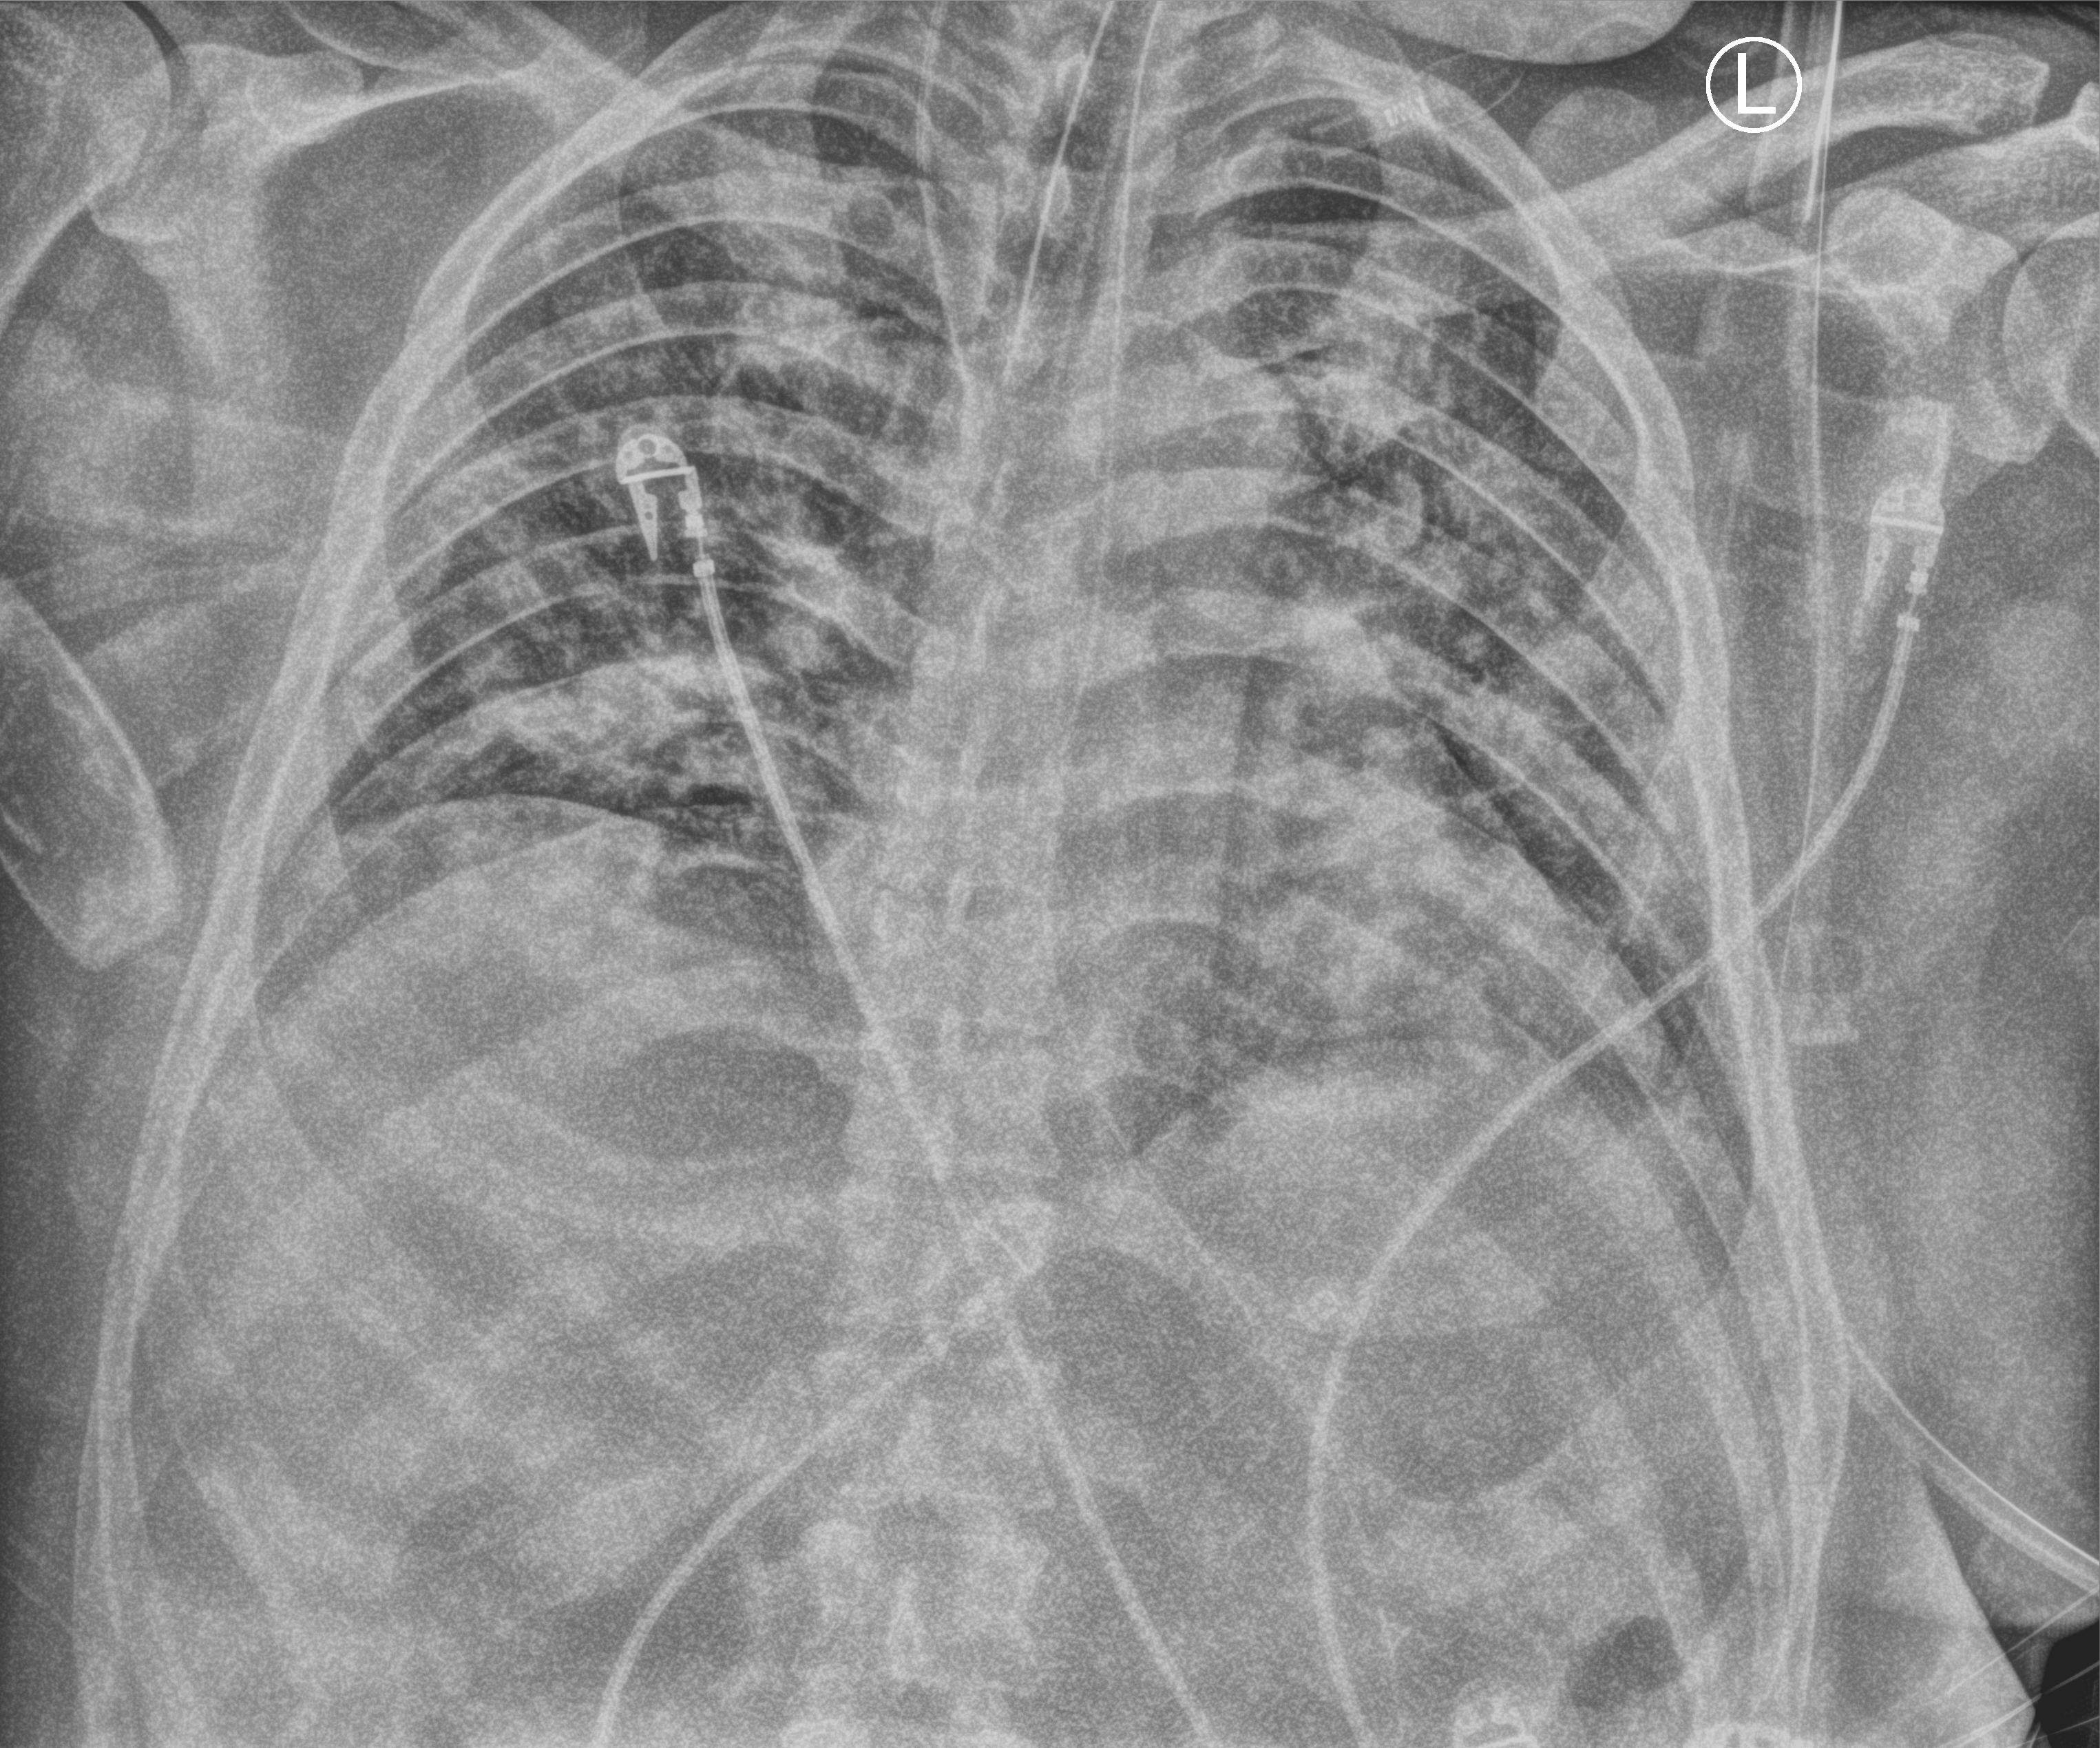
Portable chest radiograph, anteroposterior (AP) projection. Patient hospitalised with COVID-19; male, aged 18–59 years.
Admission-level facts for this patient (not findings on this image; timing relative to this image not recorded): admitted to intensive care during this hospital stay: yes; mechanically ventilated during this hospital stay: yes; length of hospital stay: 29 days.